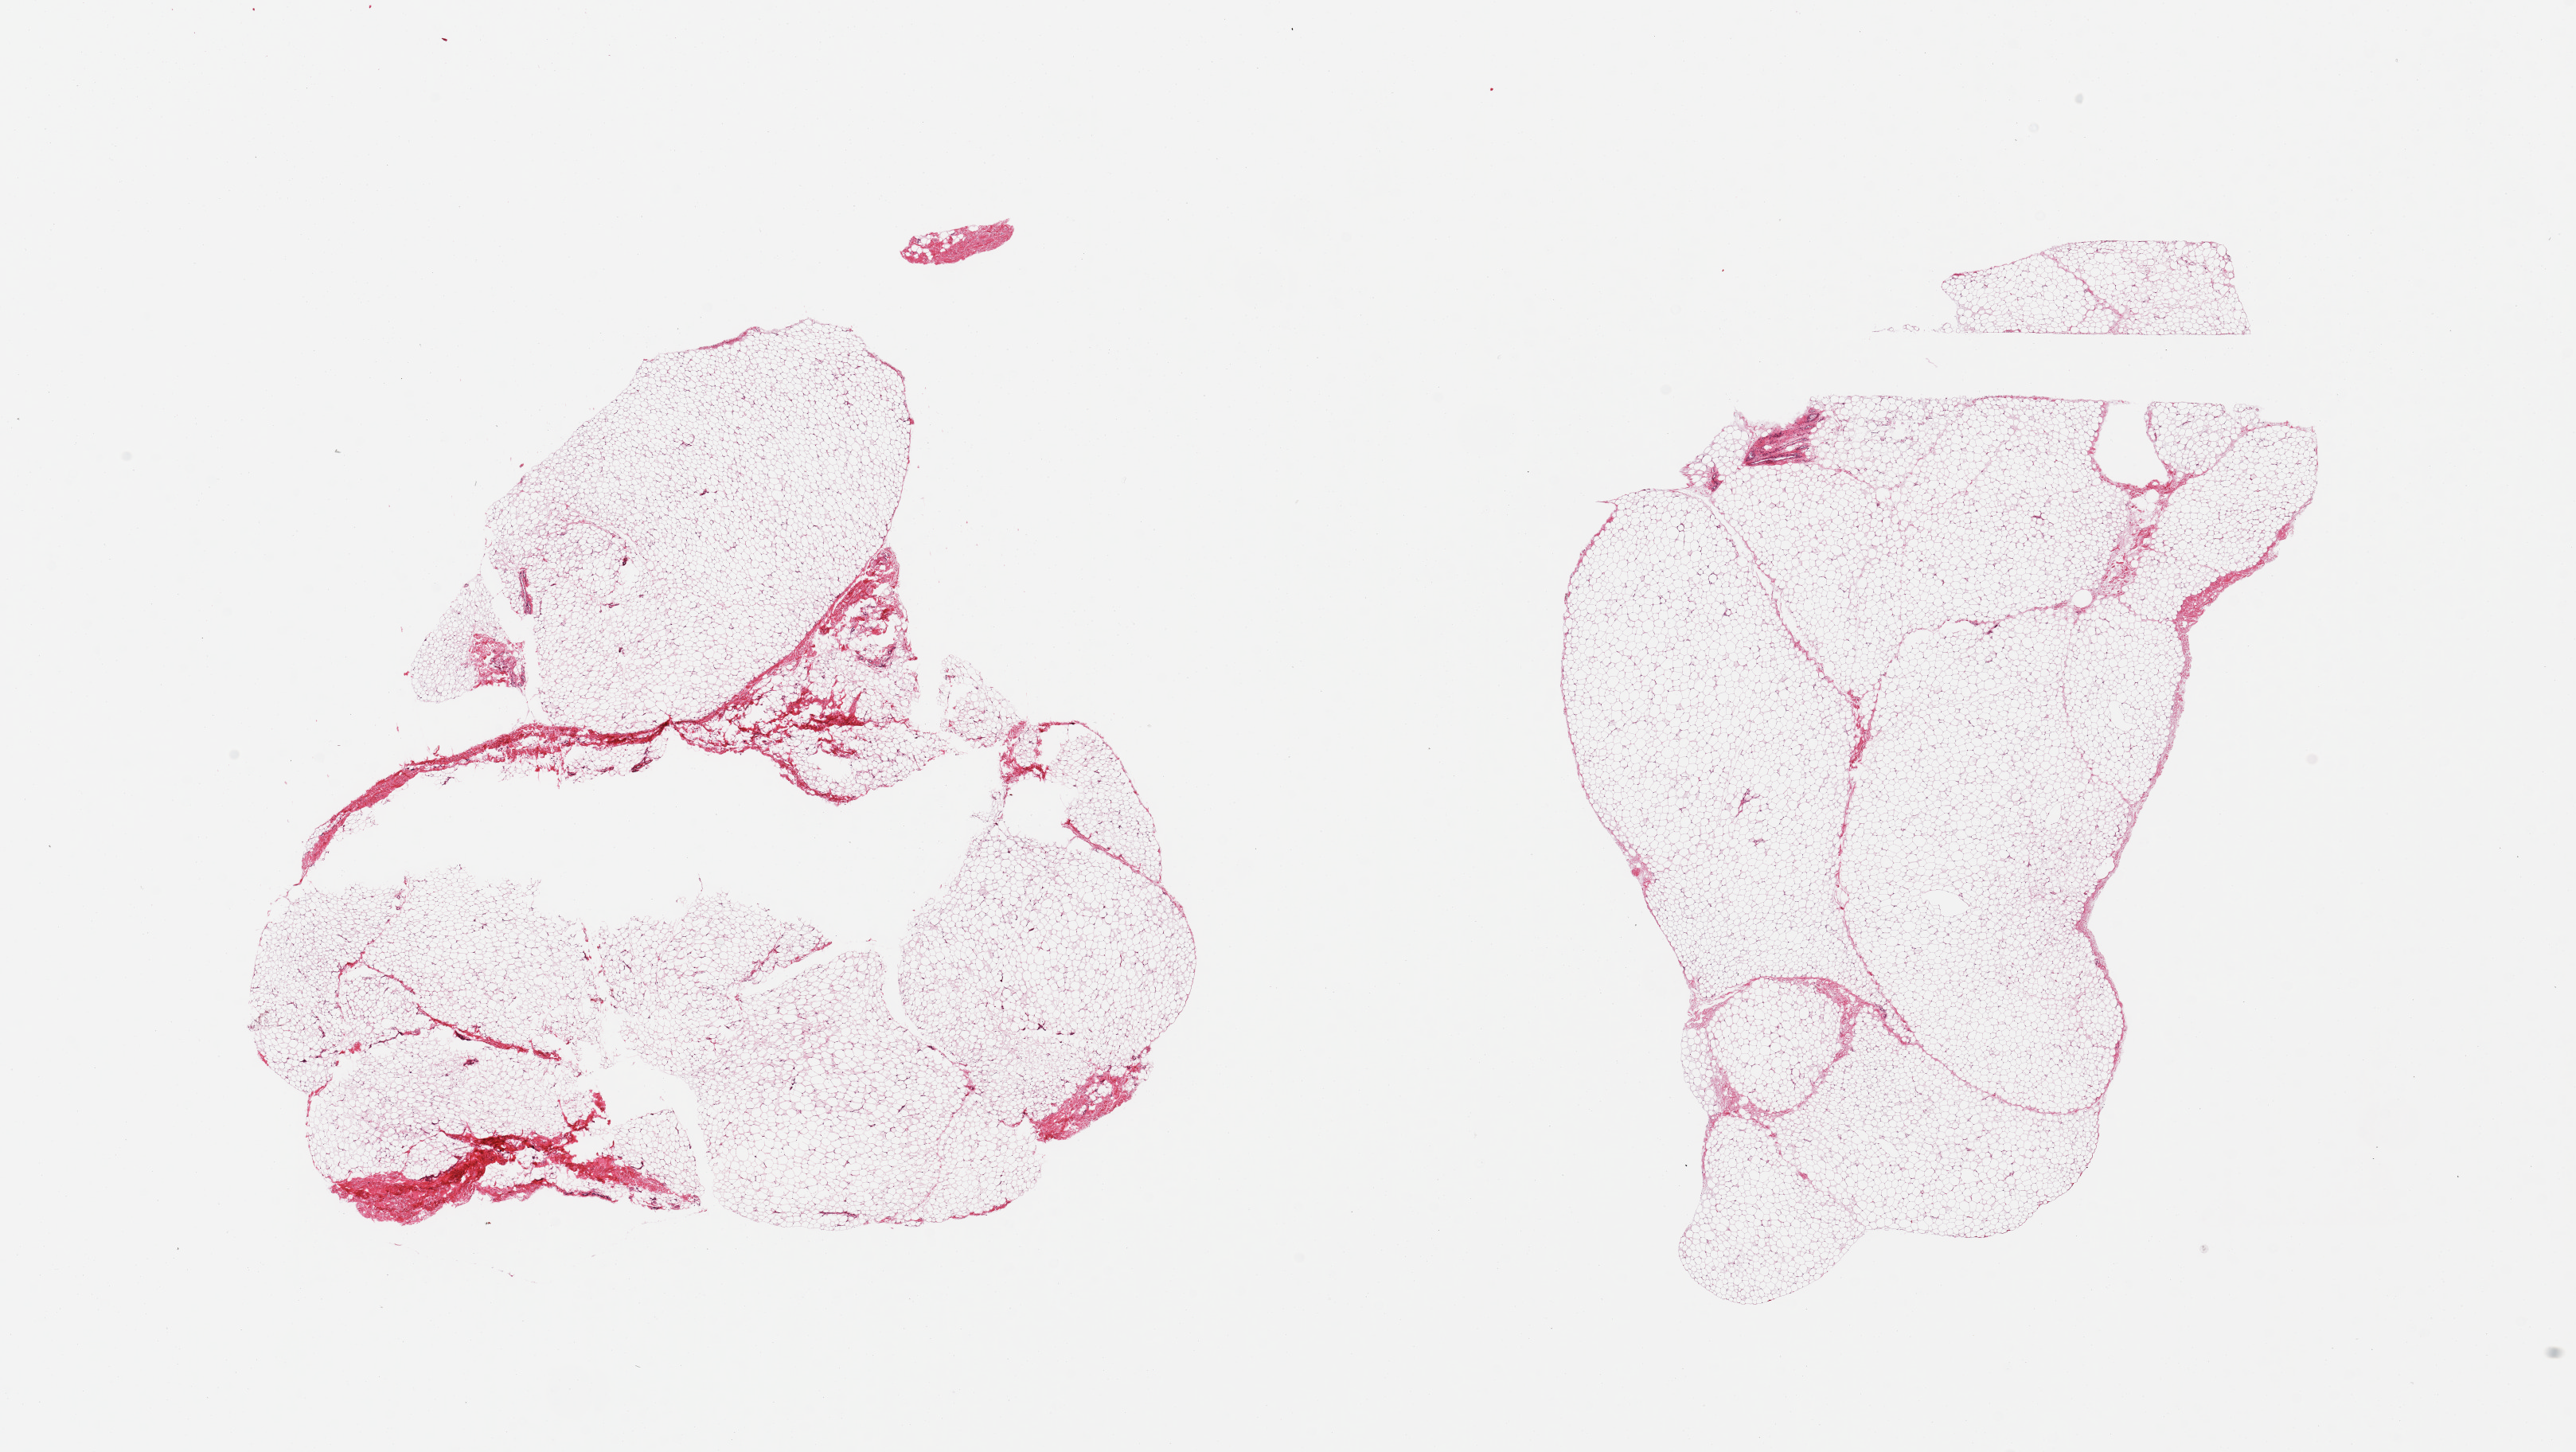
Haematoxylin and eosin whole-slide image, whole scanned area (about 25.6 x 14.4 mm) shown as a low-resolution overview; PAXgene-fixed paraffin-embedded (PFPE) section; sampled site (target tissue): breast; tissue donor sample. Male donor.
Pathologist's review note for this sample: 2 pieces; fatty tissue with less than 5% fibrous content and no mammary tissue.